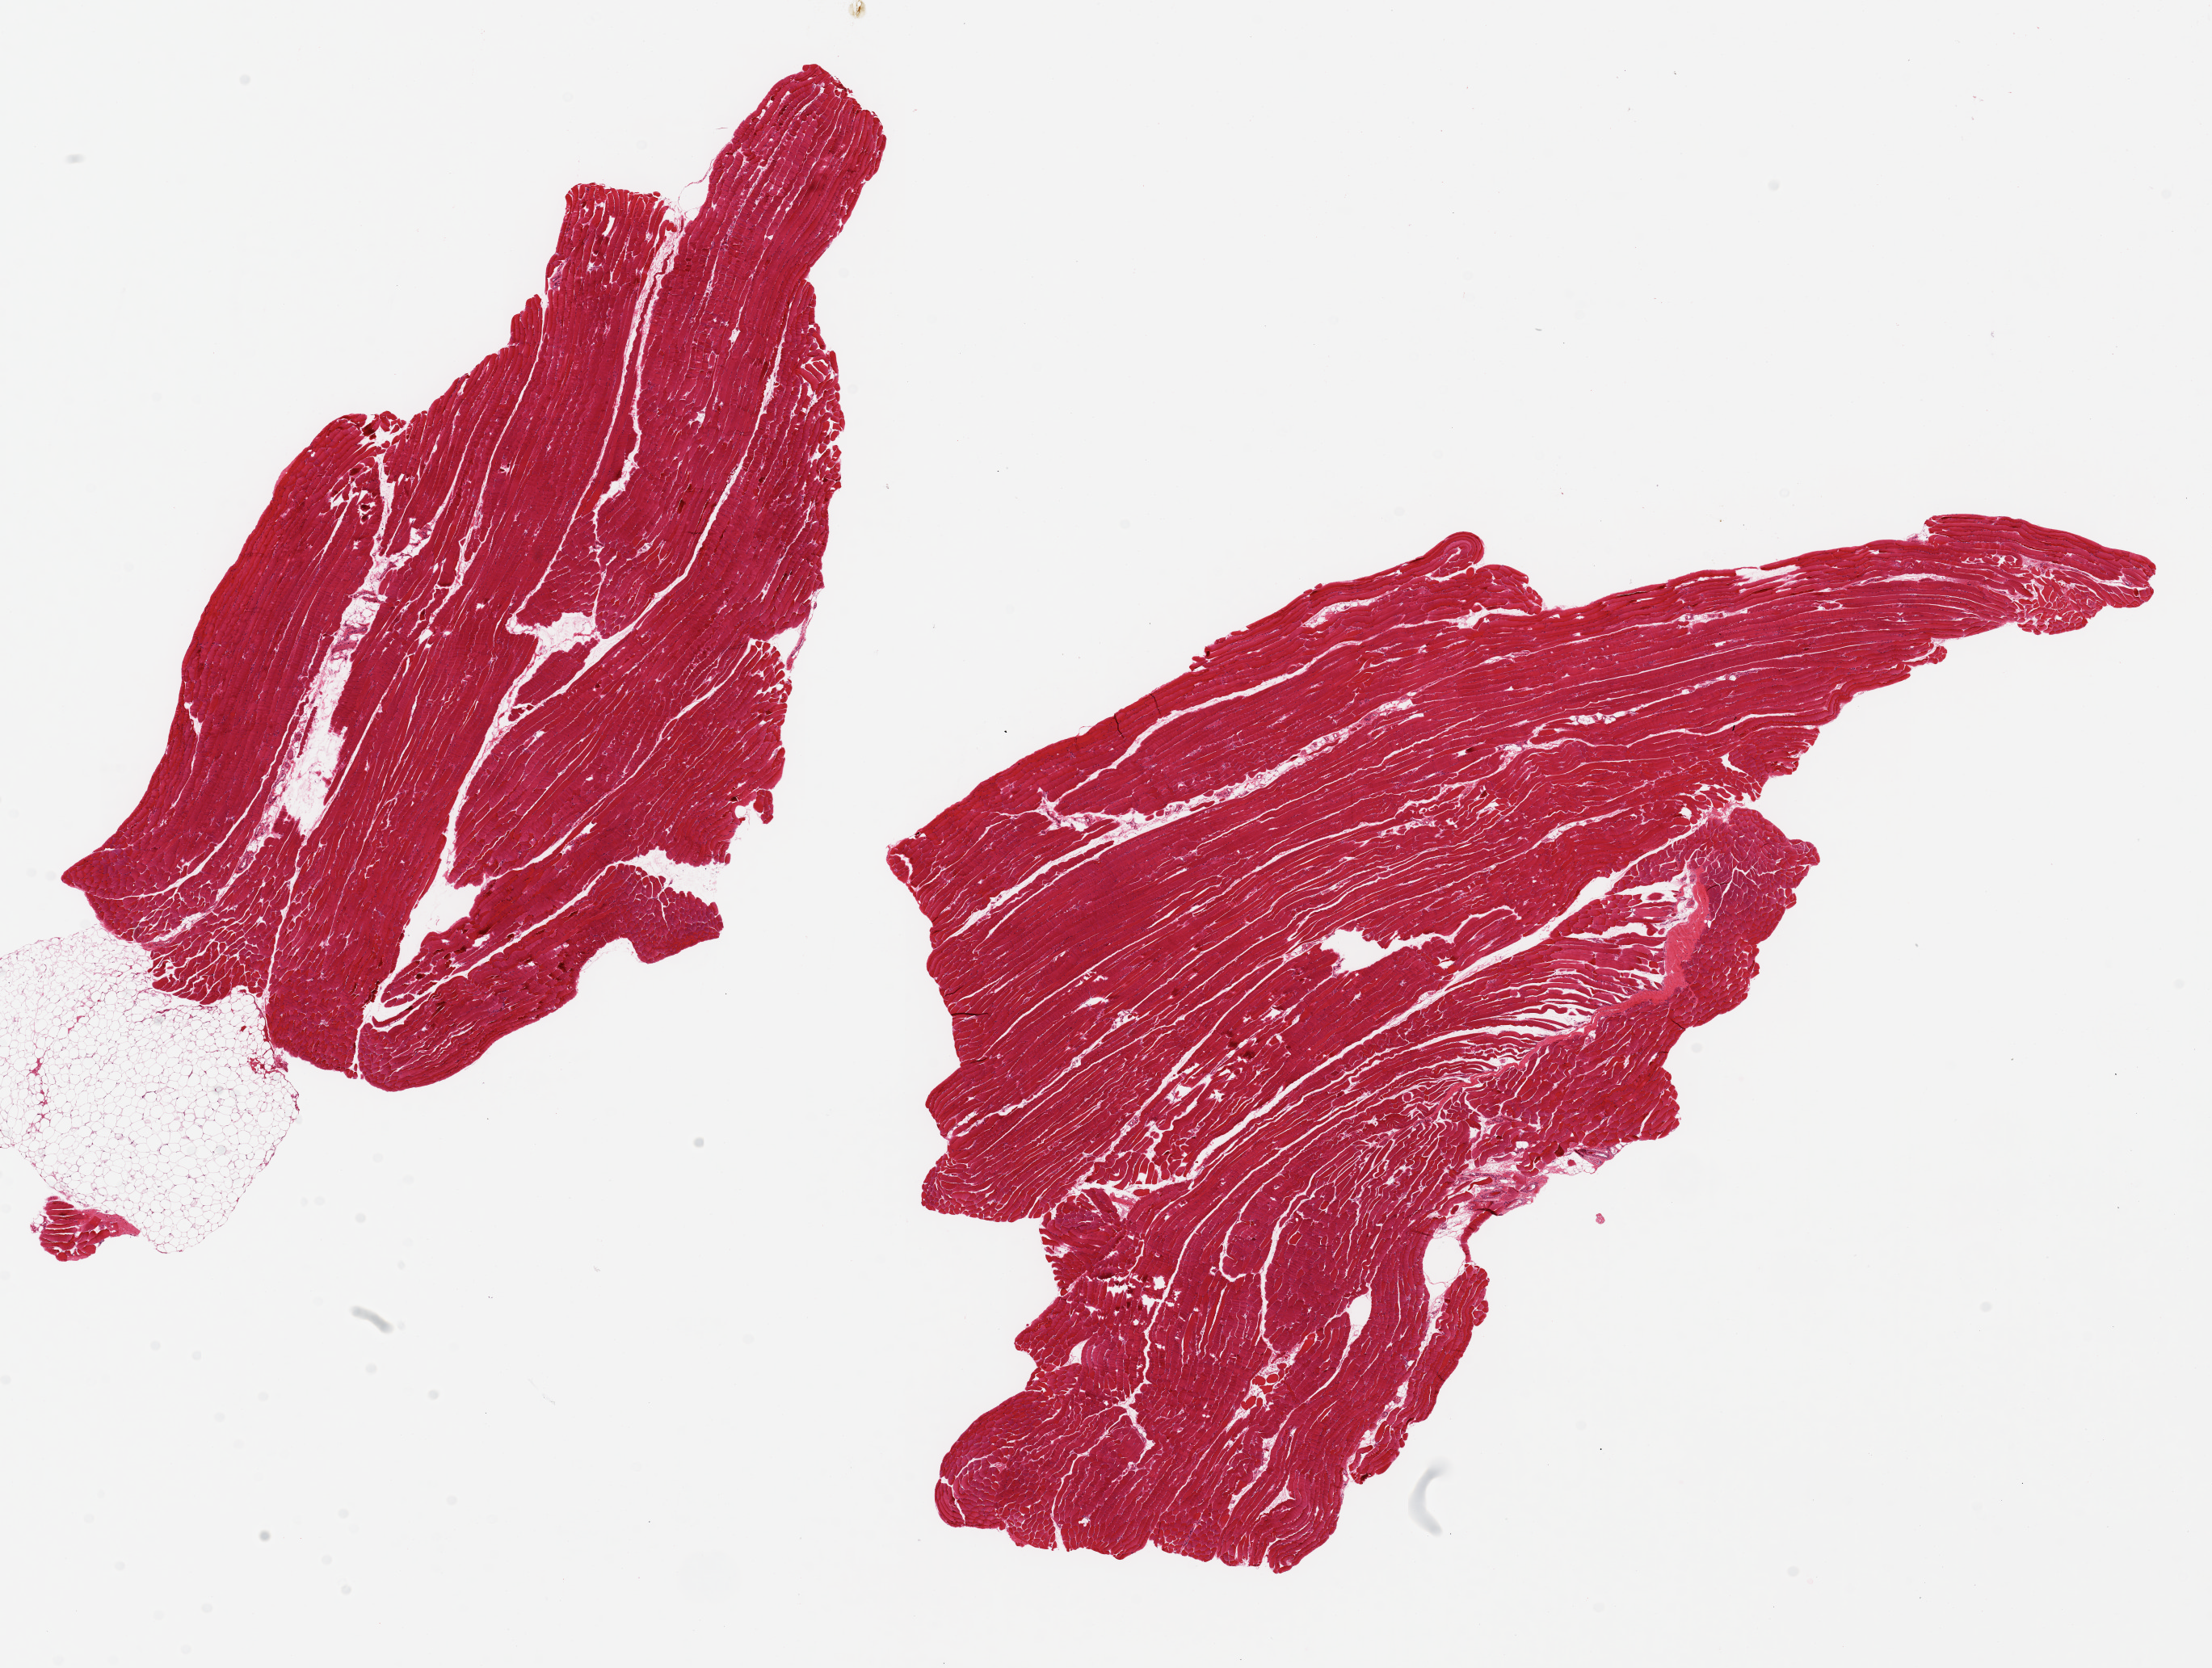
Whole-slide image, H&E stain — whole scanned area (about 21.7 x 16.3 mm, acquisition: 20x scan) shown as a low-resolution overview; PAXgene-fixed paraffin-embedded (PFPE) section; section of skeletal muscle (target tissue); donor tissue sample. Donor sex: male.
Pathologist's review note for this sample: 2 pieces, ,2% interstitial fat ~11x7mm.